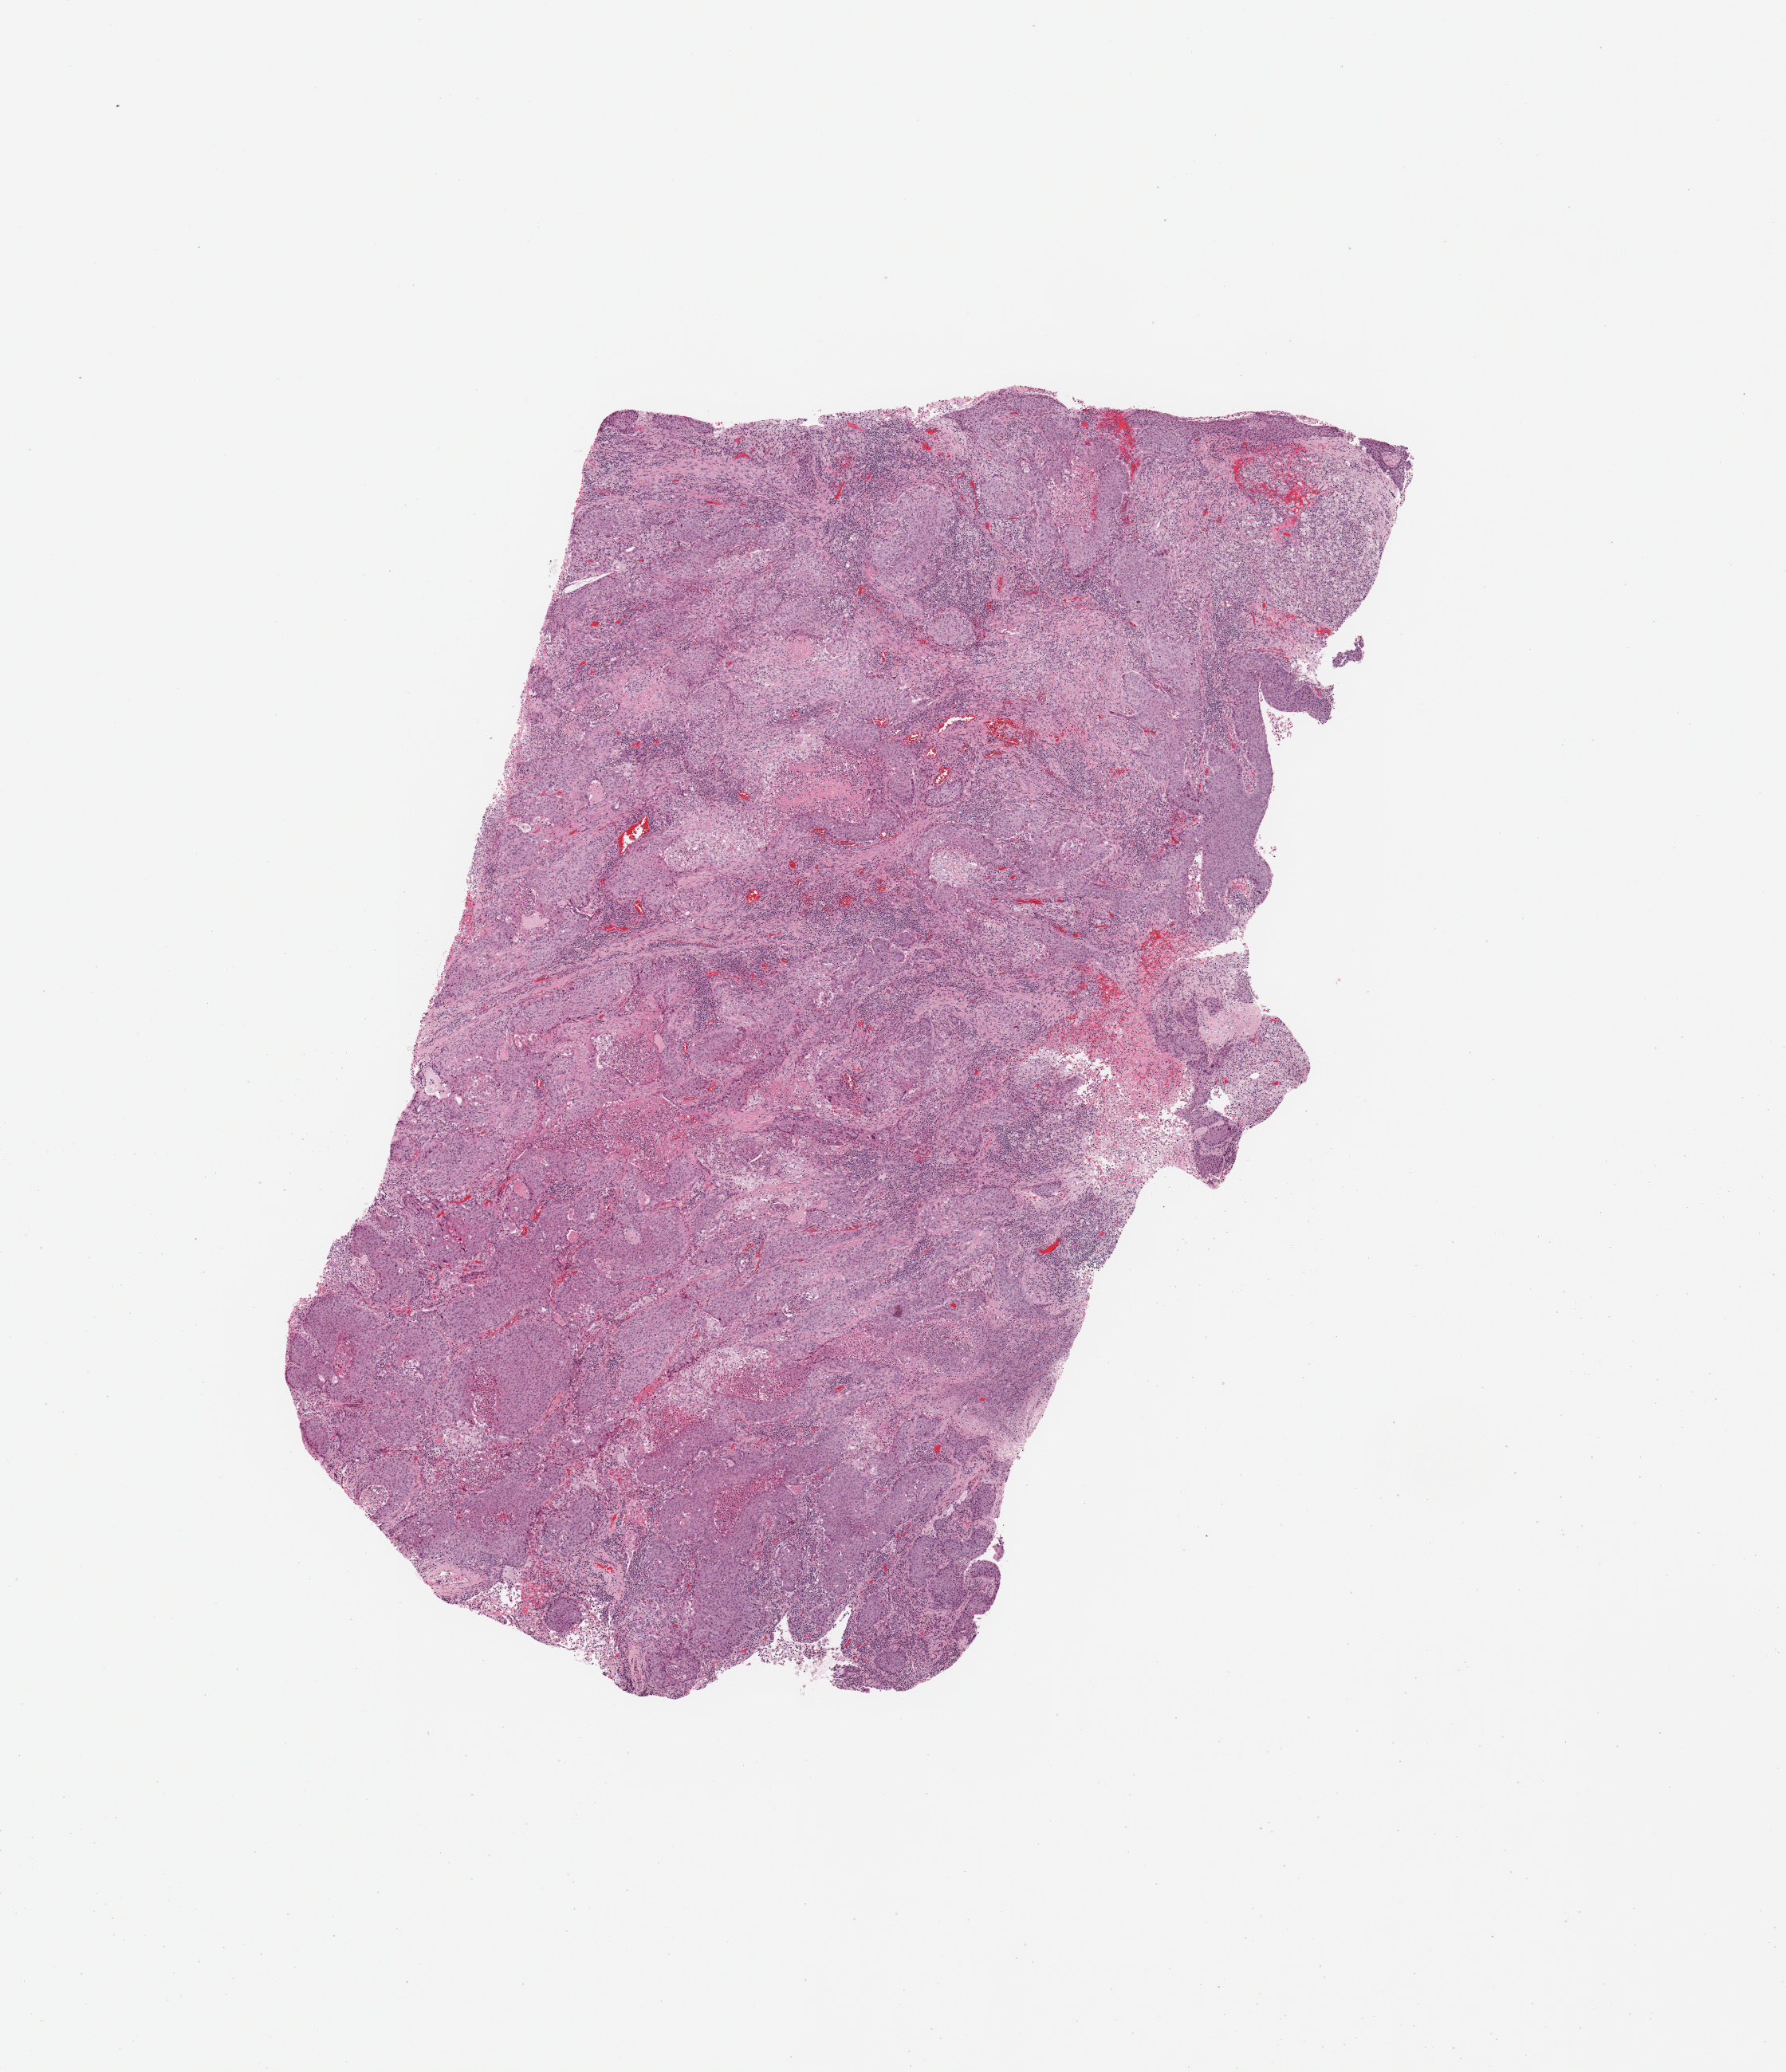
H&E whole-slide image — low-resolution overview of the scanned area, about 8.9 x 10.3 mm (from a 20x scan); lung, tumour tissue. Female, 74 y/o. Histologic grade: G2 (moderately differentiated).
Histologic diagnosis: Squamous cell carcinoma, NOS. Primary tumour site (as recorded): right upper lobe. AJCC pathologic stage: IB.